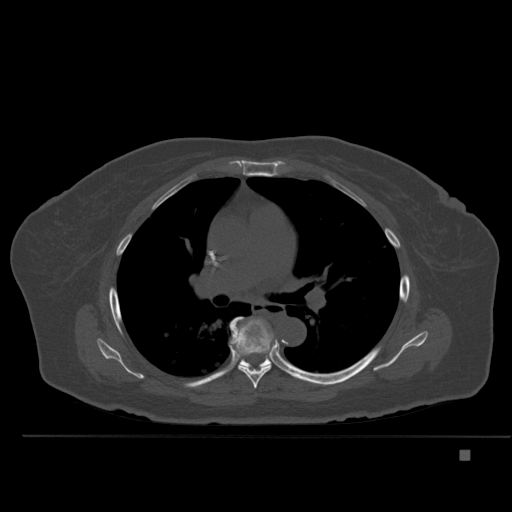
CT including the spine, one axial slice. Position 335 of 477 along the scan axis. Bone window (W 1800 / L 400 HU). 512 × 512 image matrix. Female patient, age 74 years. Case-level facts recorded for this patient, not image findings: primary cancer: colon.
Annotated regions visible in this slice (semi-automatically segmented with operator editing):
- T6 vertebra: bounding box <232,319,271,389> (left, top, right, bottom; pixels)
- T7 vertebra: <229,317,274,369>